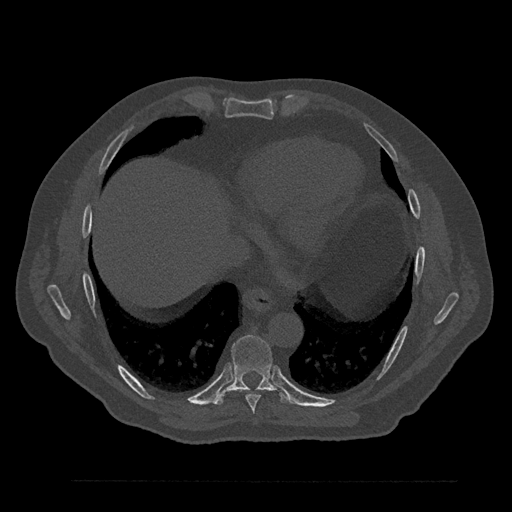
CT including the spine, one axial slice; position 427 of 797 along the scan axis; 120 kVp; bone window (W 1800 / L 400 HU); 0.5 mm slice thickness; 512 × 512 image matrix, field of view 430 × 430 mm. Patient: male, 61 years. From the clinical record (not read from this slice): primary cancer: prostate.
Annotated regions visible in this slice (semi-automatically segmented with operator editing):
- T8 vertebra: box from (x=239, y=389) to (x=260, y=413) px
- T9 vertebra: (x=214, y=335)–(x=292, y=406)